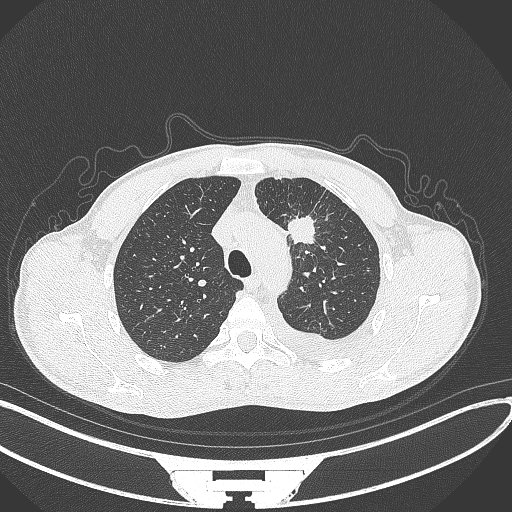
Chest CT, one axial slice. Slice 259 of 371 in the series (ordered by position). Lung window (W 1500 / L -600 HU). 1 mm slice thickness. 512 × 512 image matrix, field of view 400 × 400 mm. Male patient, age 49 years. From the clinical record (not read from this slice): clinical TNM (as recorded): T1c N1 M1.
Annotated regions visible in this slice (bounding box drawn by a radiologist):
- lung tumour (recorded histology: adenocarcinoma): bounding box [x1, y1, x2, y2] px = [287, 208, 320, 250]